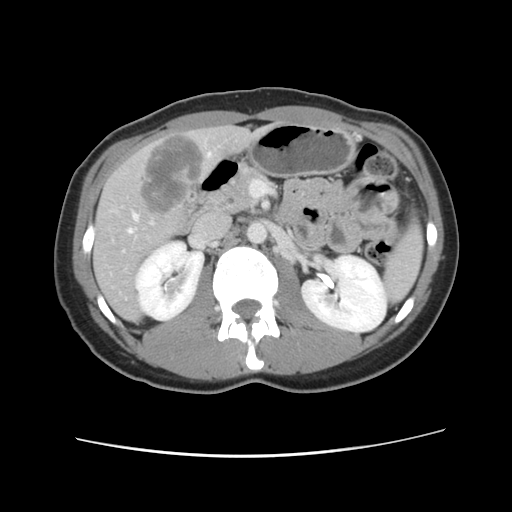
Contrast-enhanced abdominal CT, one axial slice. Slice 46 of 134 in the series (ordered by position). 120 kVp. Soft-tissue window (W 400 / L 40 HU). 2.5 mm slice thickness. 512 × 512 image matrix, field of view 339 × 339 mm. Female patient, age 33 years. From the clinical record (not read from this slice): diagnosis: colorectal cancer liver metastases, imaged before liver resection; multiple liver metastases: yes.
Outlined on this slice (outlined manually by an expert reader):
- hepatic veins: bounding box <128,153,211,234> (left, top, right, bottom; pixels)
- liver: <94,126,261,320>
- planned liver remnant (the part of the liver to remain after resection): <93,131,262,320>
- liver metastasis: <138,136,205,217>